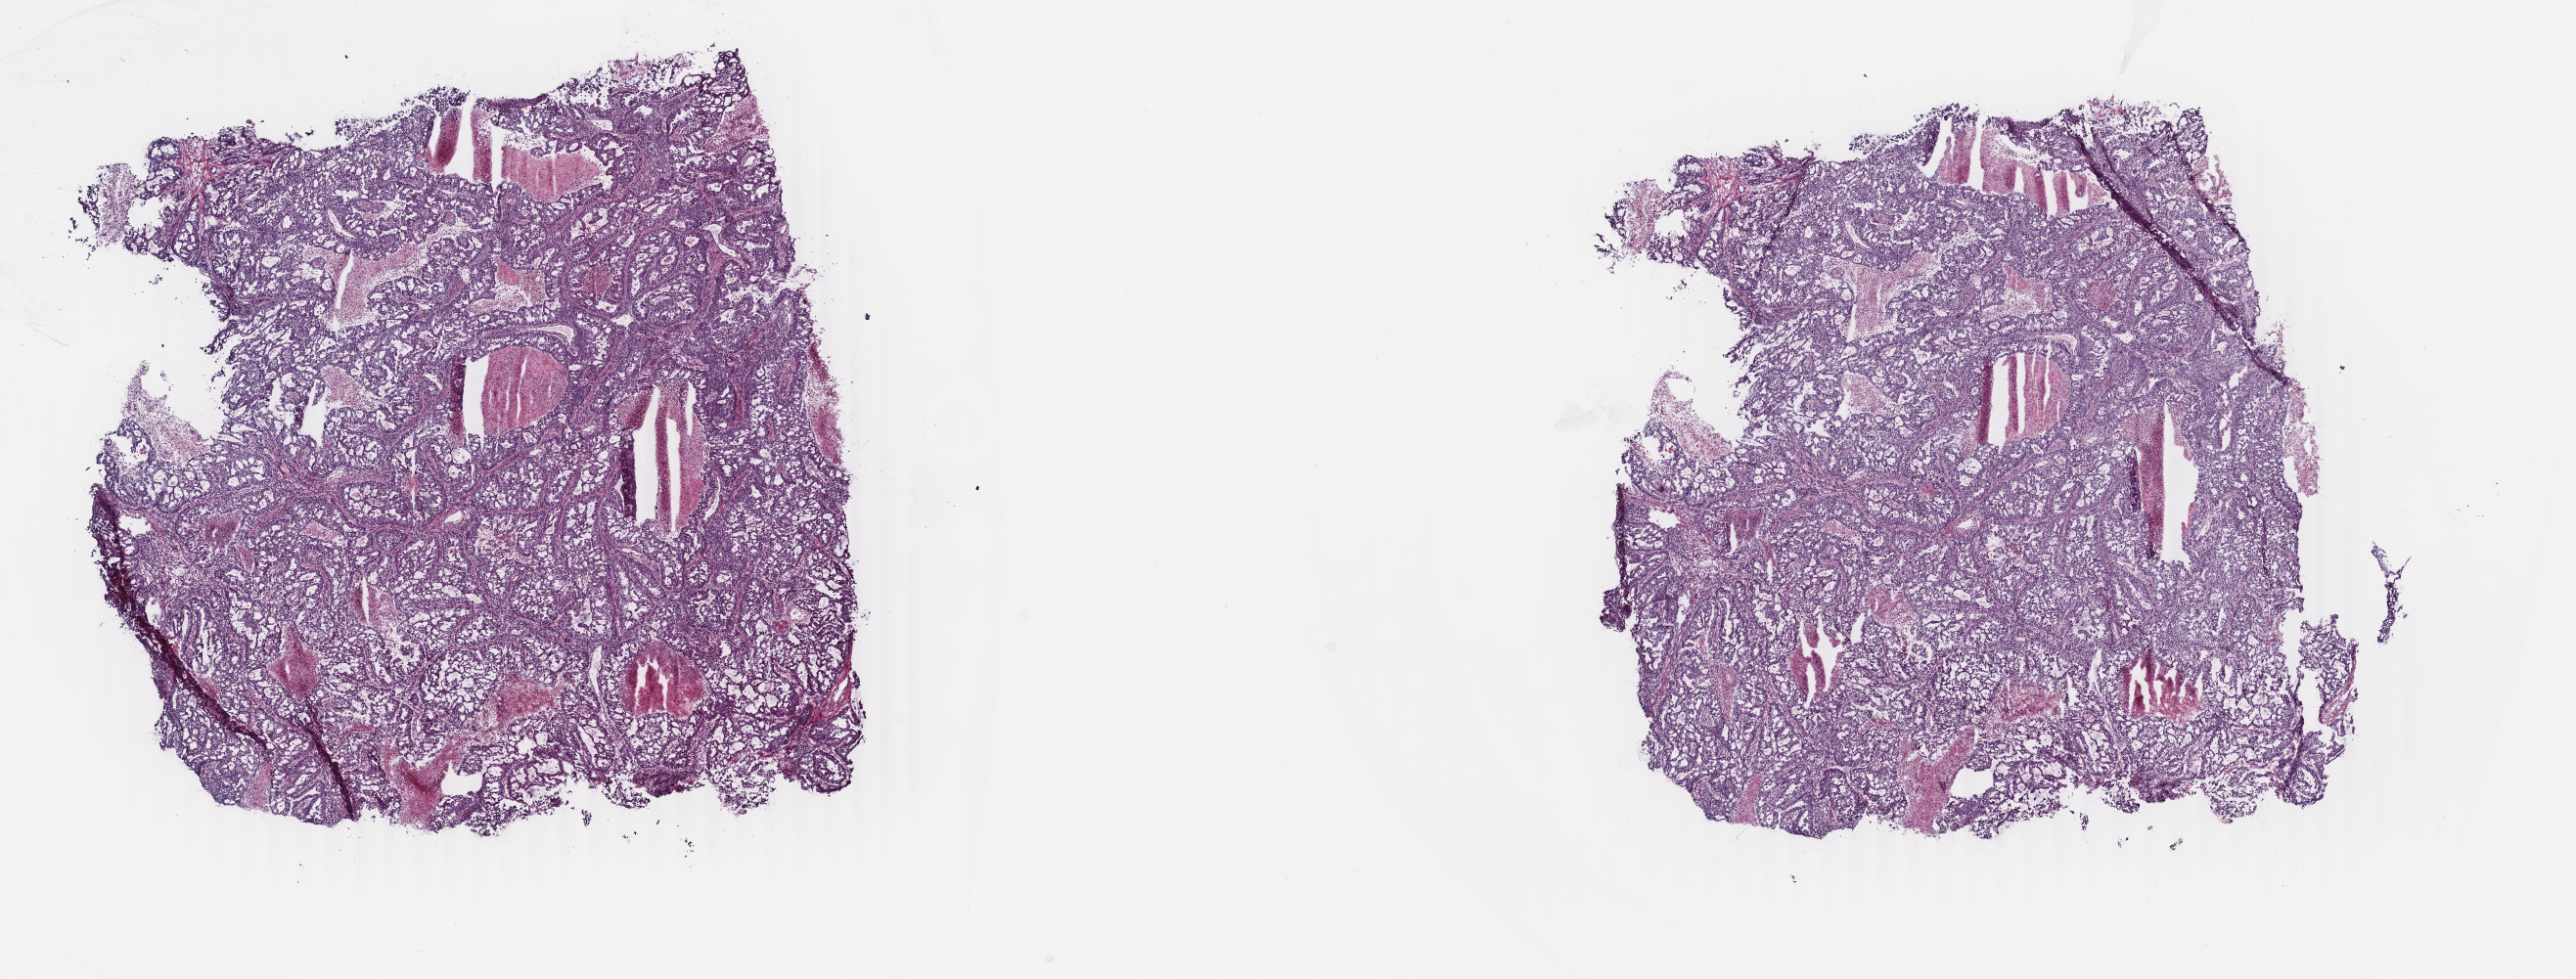
Digitized H&E tissue section (whole slide), a low-resolution overview of the entire scanned area, about 20.9 x 8.0 mm, frozen section, primary tumour sample from the lung. Male, age 56 years at initial diagnosis. Pathologist review of this section (percent, as recorded): tumour cells 80%, tumour nuclei 88%, normal cells 0%, stromal cells 0%, necrosis 20%. Infiltration values recorded for this section: lymphocyte infiltration 0%, monocyte infiltration 0%, neutrophil infiltration 0%.
- histologic diagnosis: Adenocarcinoma, NOS
- AJCC pathologic stage: IIA (7th edition)